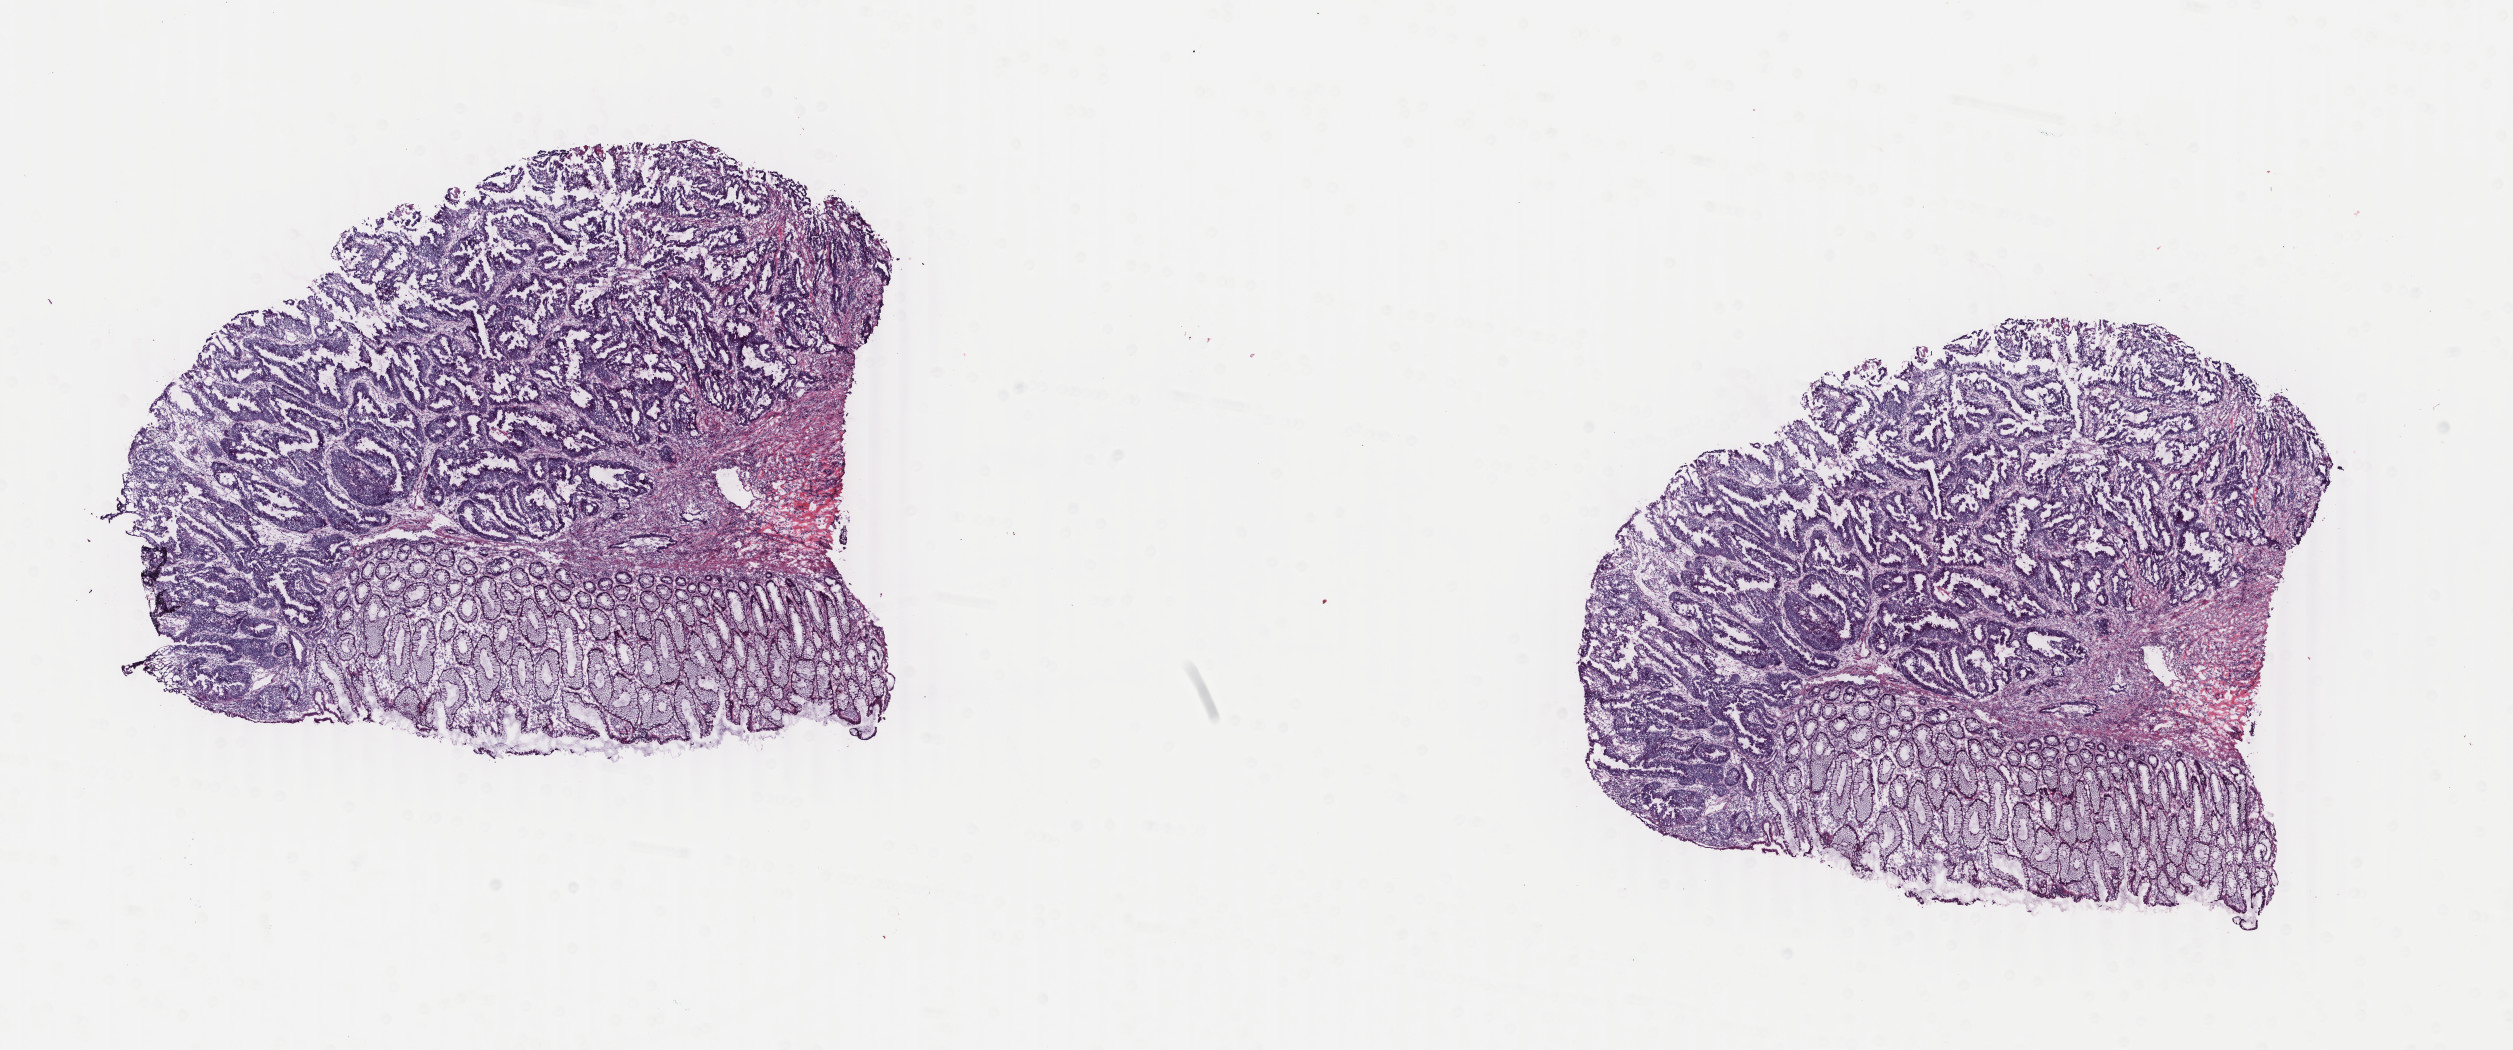
H&E-stained whole-slide image — whole scanned area (about 20.0 x 8.4 mm) shown as a low-resolution overview, frozen section from the bottom of the tissue portion, primary tumour sample from the colon. Female patient; age at initial diagnosis 63 years. Slide review estimates, as recorded: tumour cells 65%, tumour nuclei 65%, normal cells 22%, stromal cells 13%, necrosis 0%. Infiltration values recorded for this section: lymphocyte infiltration 2%, monocyte infiltration 0%, neutrophil infiltration 0%.
Pathologic diagnosis: Adenocarcinoma, NOS (sigmoid colon). Lymph nodes positive (case pathology): 1 of 15 examined. AJCC pathologic stage: III (5th edition). TNM: T3 N1 M0.